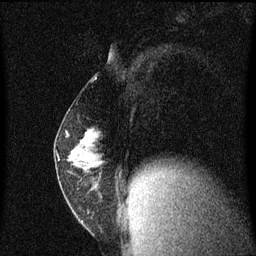
Breast MRI (dynamic contrast-enhanced), one sagittal slice. Slice 29 of 60 in the series (ordered by position). Dynamic contrast-enhanced series, image 2 of 3 at this slice position (ordered by acquisition). 1.5 T. TE 4.2 ms, TR 8.4 ms. 256 × 256 image matrix, field of view 200 × 200 mm. Patient: female, 52 years. From the clinical record (not read from this slice): setting: breast cancer imaged before/during neoadjuvant chemotherapy; receptor status: HER2-positive.
Annotated regions visible in this slice (semi-automatically segmented with operator editing):
- analysis volume of interest (the breast-tissue region the enhancement analysis was run in; not a lesion): box from (x=55, y=124) to (x=119, y=191) px
- tumour enhancement mask (voxels above the 70 % enhancement threshold inside the analysis volume of interest): (x=70, y=128)–(x=98, y=157)